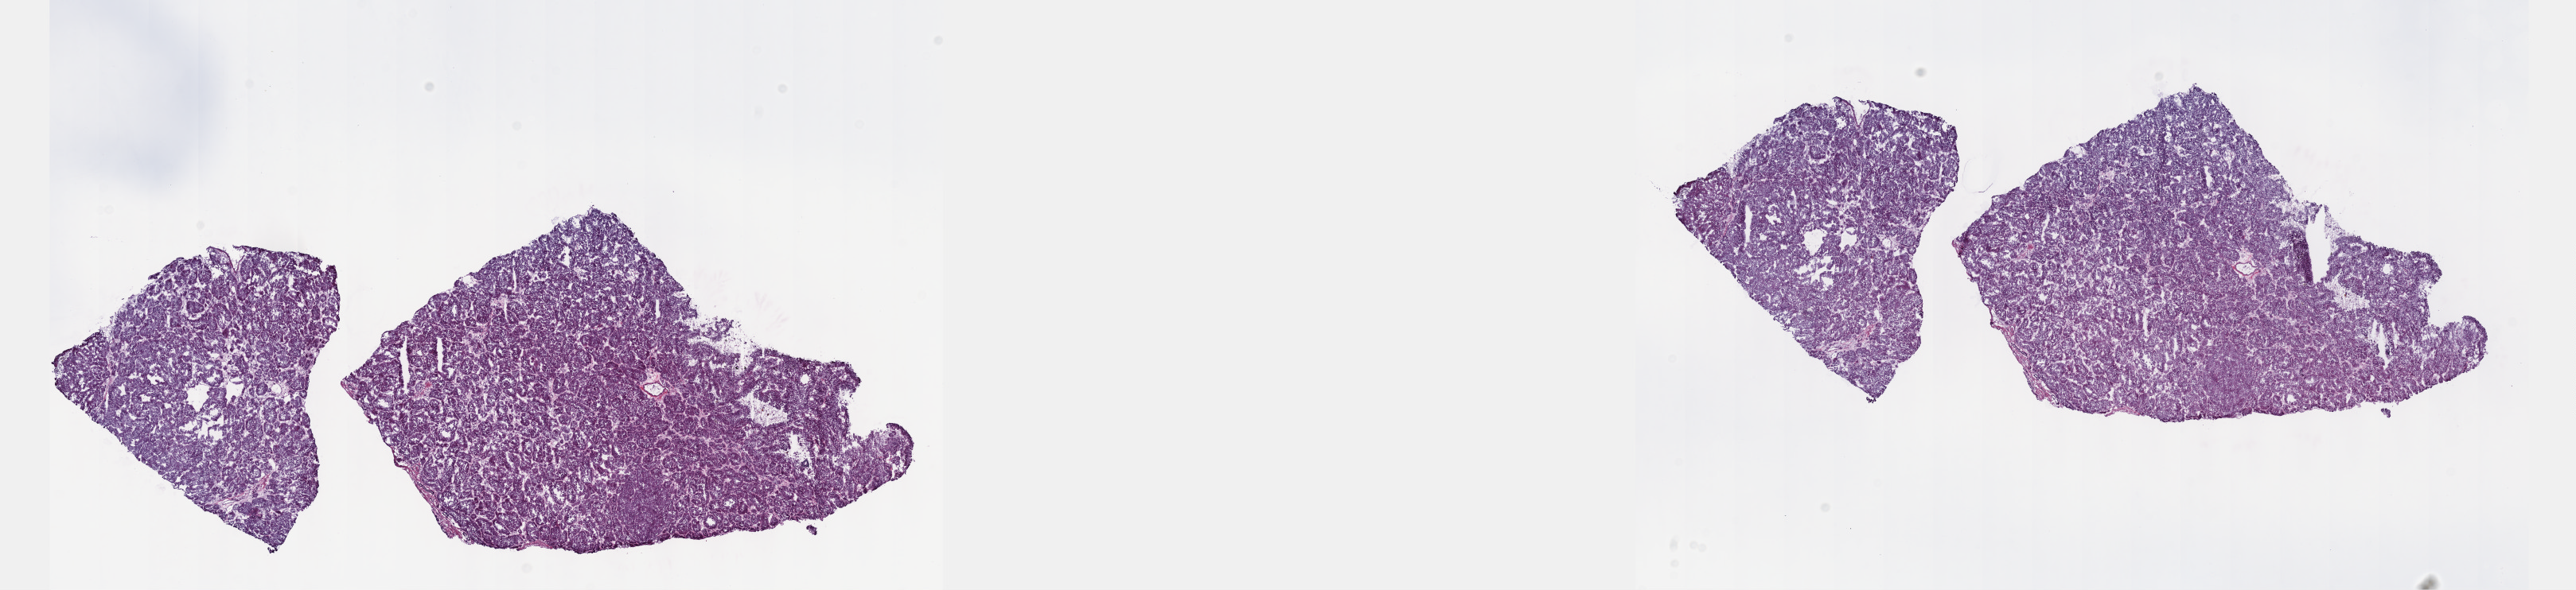
Hematoxylin and eosin (H&E) stained whole-slide image — shown as a low-resolution overview of the whole scanned area (about 26.2 x 6.0 mm, acquisition: 40x scan); frozen section from the top of the tissue portion; primary tumour sample from the kidney. Female, age 56 years at initial diagnosis. Pathologist review of this section (percent, as recorded): tumour cells 100%, tumour nuclei 80%, normal cells 0%, stromal cells 0%, necrosis 0%. Inflammatory infiltration, as recorded: lymphocyte infiltration 1%, monocyte infiltration 2%, neutrophil infiltration 0%.
Pathologic diagnosis: Papillary adenocarcinoma, NOS. AJCC pathologic stage: I (7th edition). TNM: T1b N0 MX.